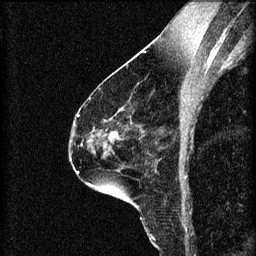
Breast MRI (dynamic contrast-enhanced), one sagittal slice; slice 38 of 60 in the series (ordered by position); 3 images stored at this slice position (order not interpretable as contrast timing); 1.5 T; TE 4.2 ms, TR 8.2 ms; 2 mm slice thickness; 256 × 256 image matrix, field of view 180 × 180 mm. Patient: female, 60 years.
Outlined on this slice (semi-automatic segmentation, software-assisted and operator-edited):
- analysis volume of interest (the breast-tissue region the enhancement analysis was run in; not a lesion): bounding box (x1, y1, x2, y2) in pixels: (89, 118, 125, 151)
- tumour enhancement mask (voxels above the 70 % enhancement threshold inside the analysis volume of interest): (110, 132, 118, 137)